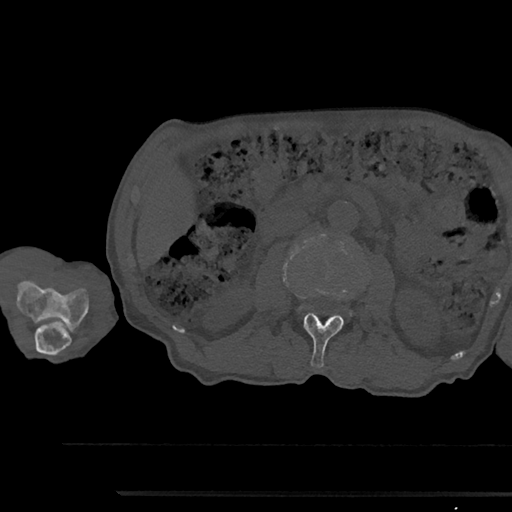
CT including the spine, one axial slice; position 537 of 797 along the scan axis; reconstruction kernel Br40s/3; 120 kVp; bone window (W 1800 / L 400 HU); 0.5 mm slice thickness; 512 × 512 image matrix. Patient: male, 79 years. From the clinical record (not read from this slice): primary cancer: prostate.
Structures marked on this image (semi-automatically segmented with operator editing):
- L2 vertebra: bounding box <304,312,344,367> (left, top, right, bottom; pixels)